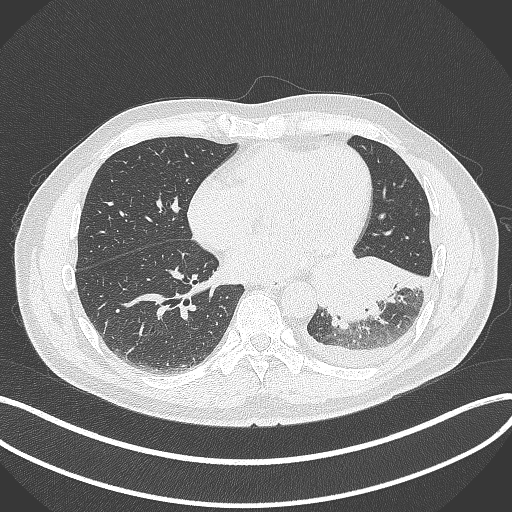
Chest CT, one axial slice; slice 139 of 342 in the series (ordered by position); reconstruction kernel B70f; lung window (W 1500 / L -600 HU); 1 mm slice thickness; 512 × 512 image matrix, field of view 400 × 400 mm. Male patient, age 58 years. Case-level facts recorded for this patient, not image findings: clinical TNM (as recorded): T3 N1 M1b.
Annotated regions visible in this slice (rectangle marked by the reading radiologist):
- lung tumour (recorded histology: small cell carcinoma): bounding box (x1, y1, x2, y2) in pixels: (311, 246, 425, 333)